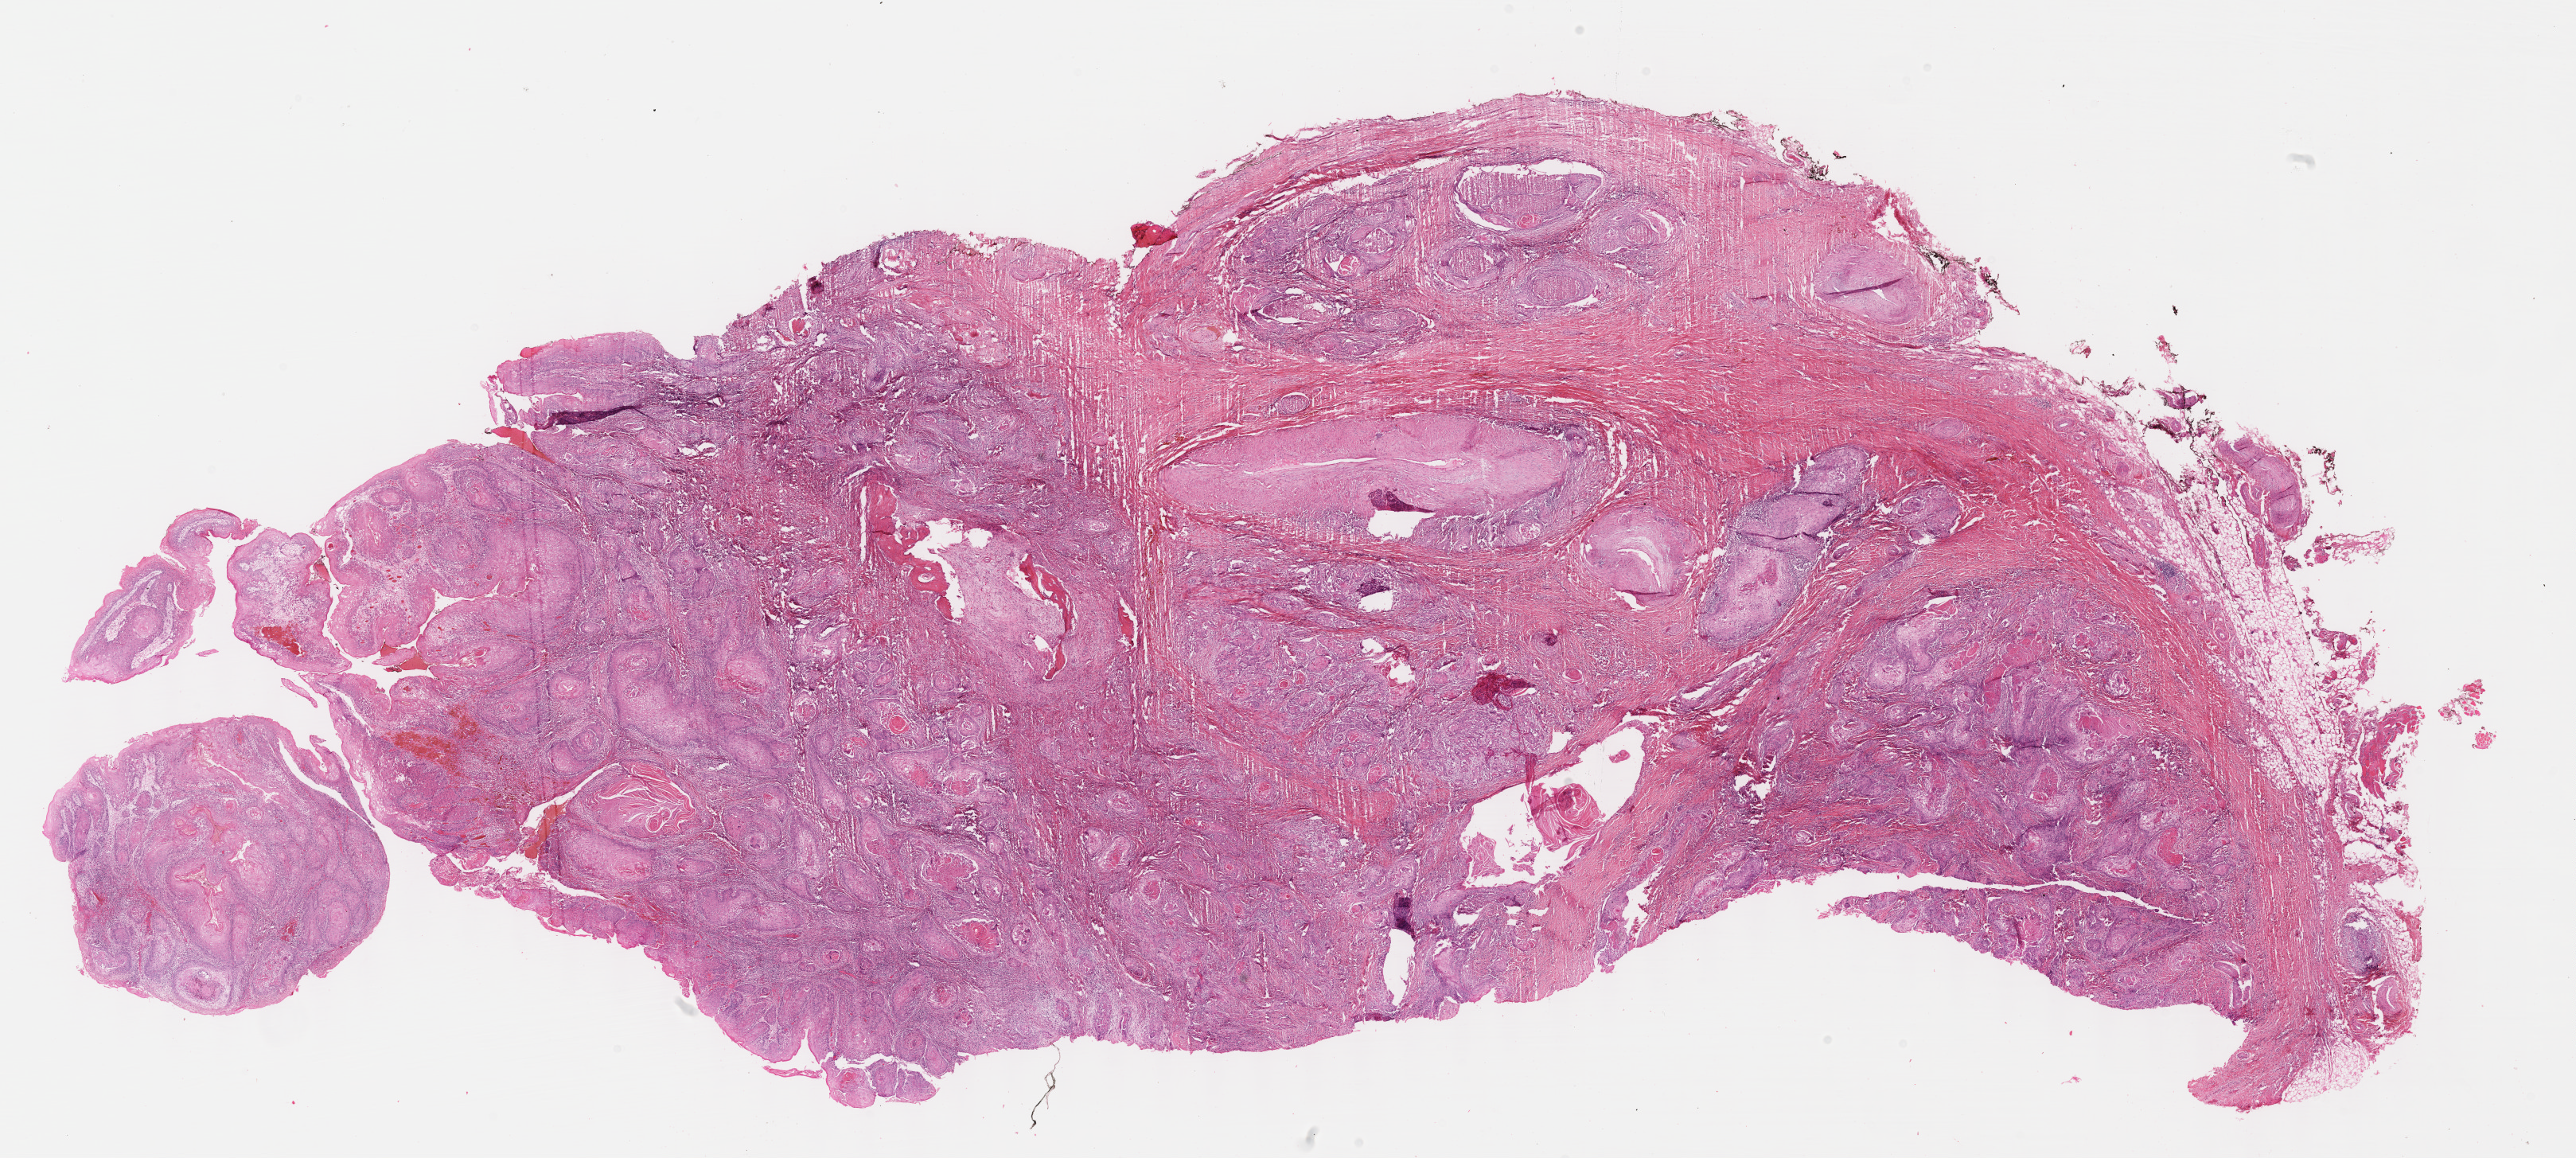
Hematoxylin and eosin (H&E) stained whole-slide image, whole scanned area (about 26.2 x 11.8 mm) shown as a low-resolution overview, formalin-fixed paraffin-embedded (FFPE) diagnostic section, head and neck, primary tumour sample. Male patient; age at initial diagnosis 87 years. Histologic grade: G1 (well differentiated).
Pathologic diagnosis: Squamous cell carcinoma, NOS (overlapping lesion of lip, oral cavity and pharynx). AJCC pathologic stage: II.